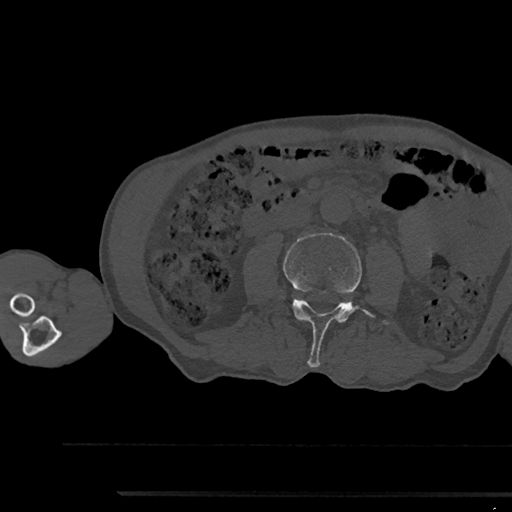
CT including the spine, one axial slice; position 482 of 797 along the scan axis; bone window (W 1800 / L 400 HU); 0.5 mm slice thickness; 512 × 512 image matrix. Patient: male, 79 years. From the clinical record (not read from this slice): primary cancer: prostate.
Outlined on this slice (semi-automatically segmented with operator editing):
- L3 vertebra: bounding box <283,233,374,367> (left, top, right, bottom; pixels)